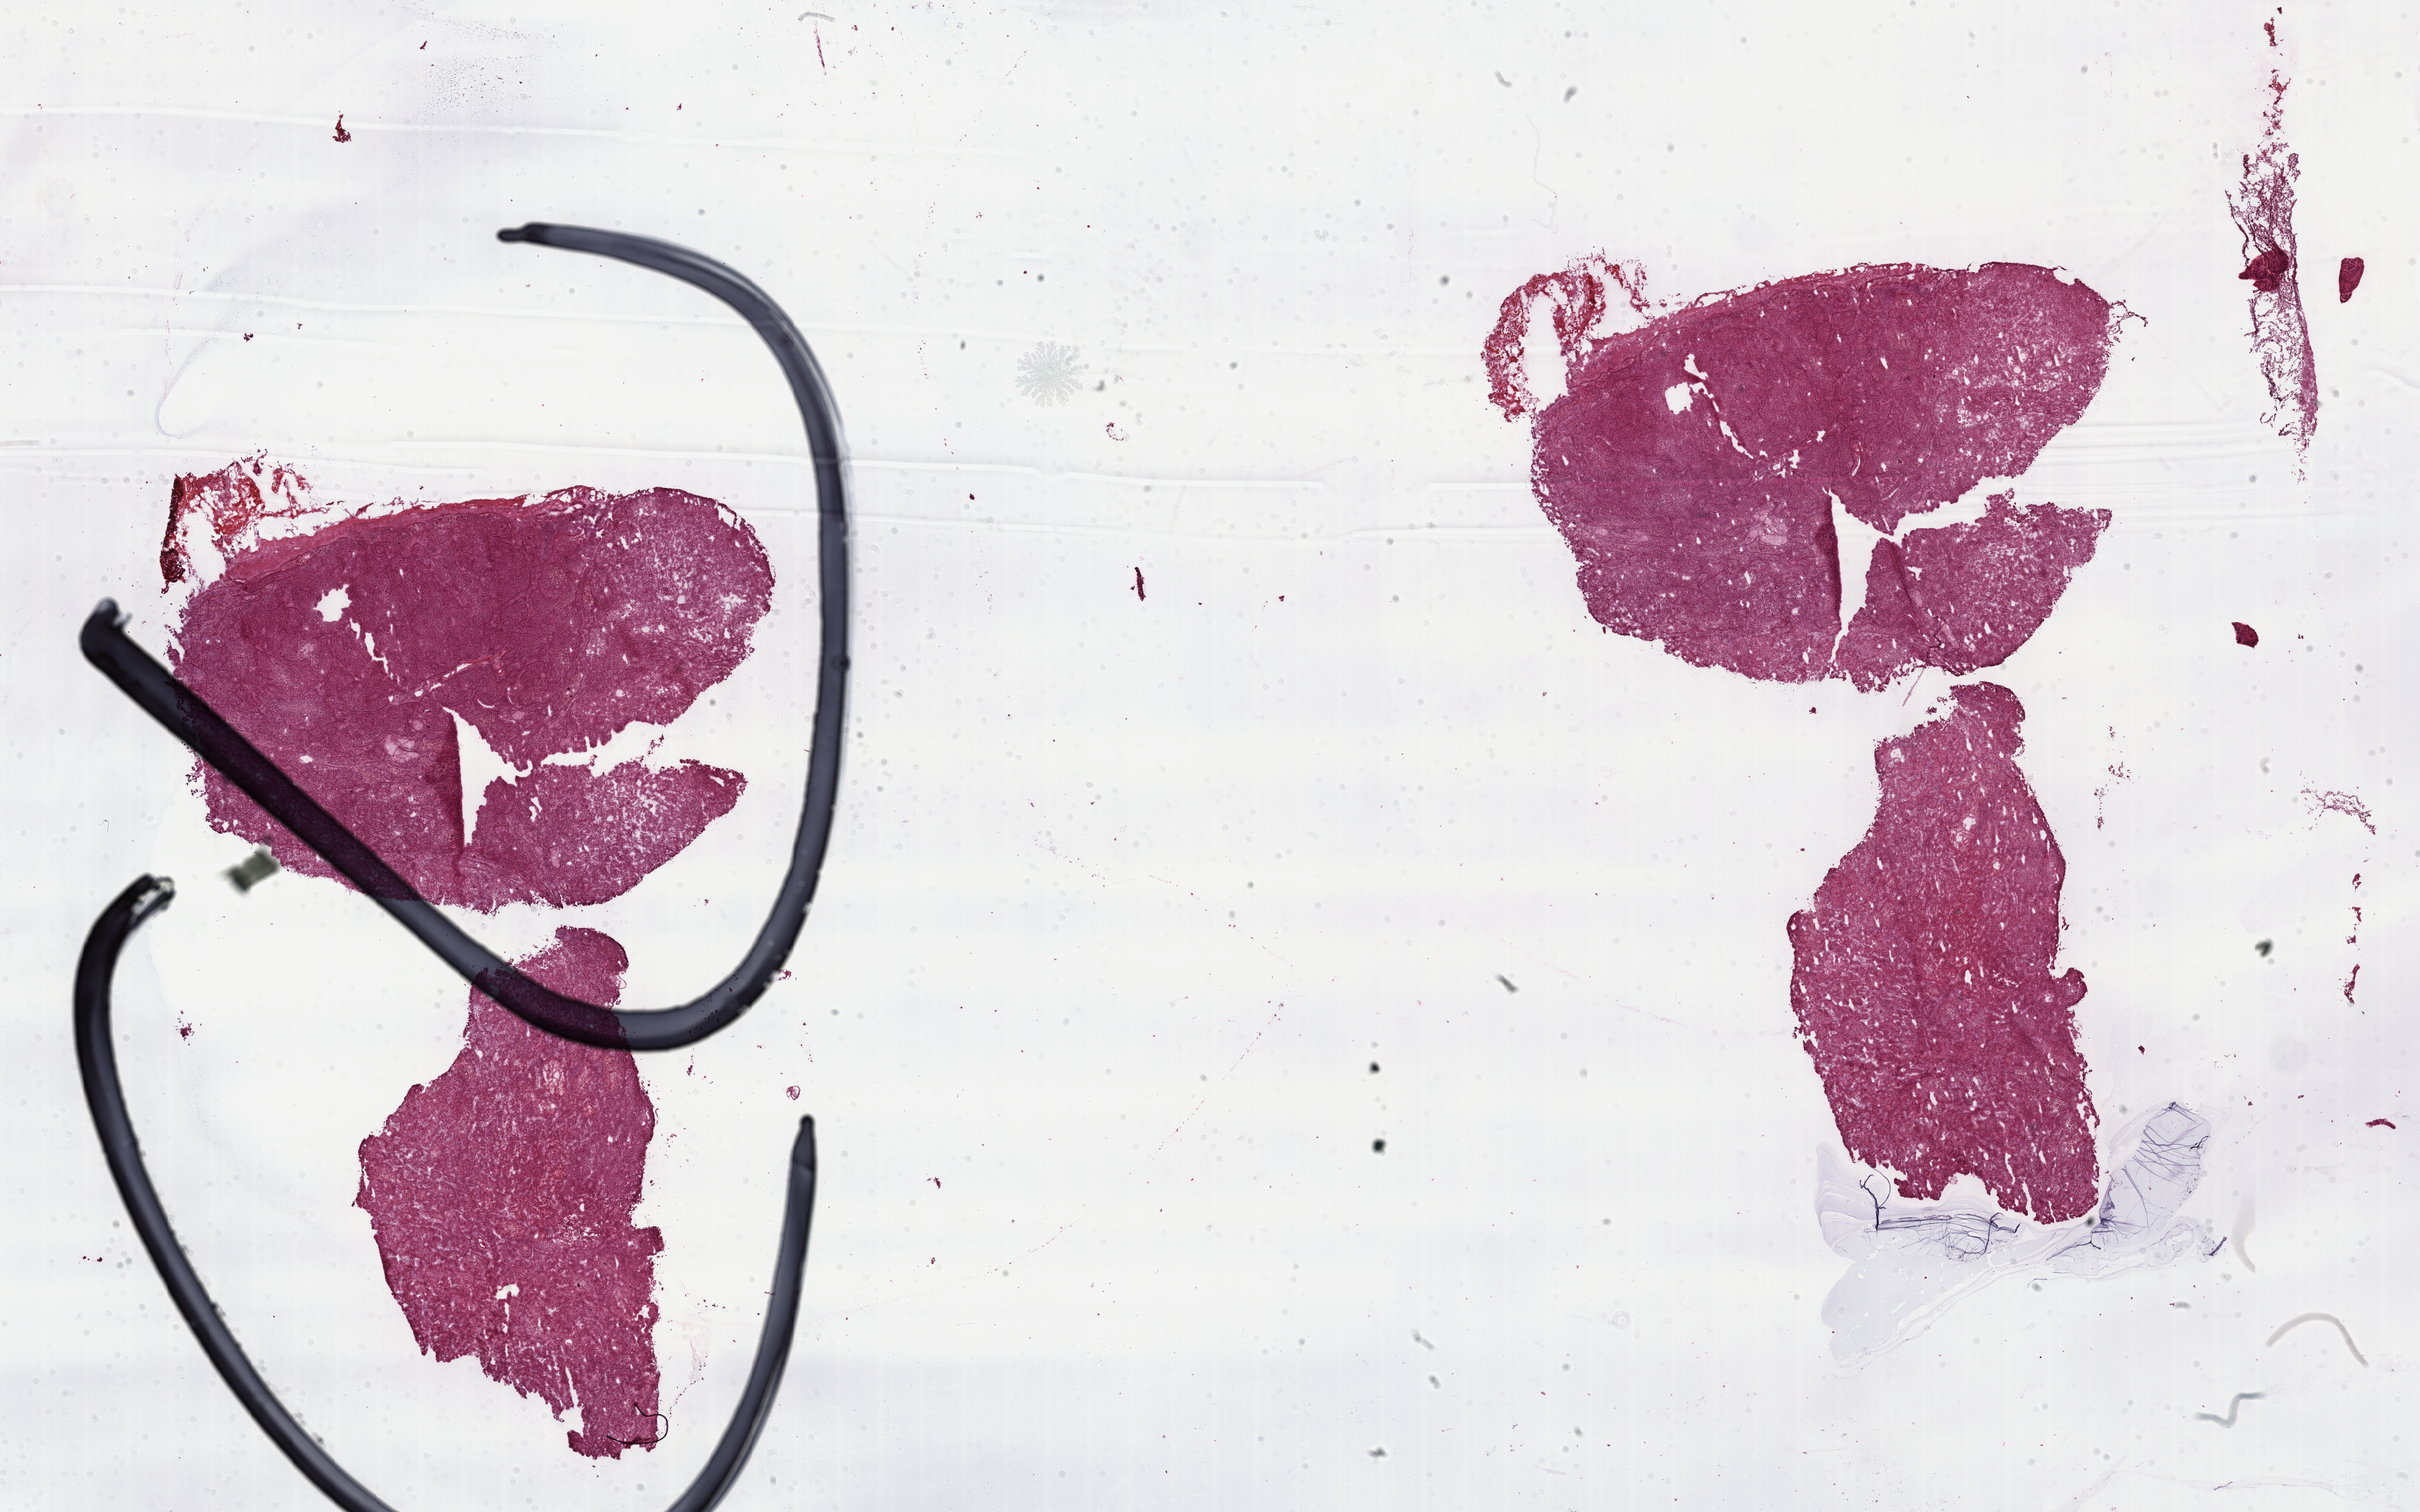
H&E whole-slide image, low-resolution overview of the scanned area, about 29.2 x 18.2 mm (acquisition: 40x scan); frozen section from the top of the tissue portion; sample: primary tumour, kidney. Male, age 61 years at initial diagnosis. Composition of this section per pathologist review: tumour cells 100%, tumour nuclei 70%, normal cells 0%, stromal cells 0%, necrosis 0%. Infiltration values recorded for this section: lymphocyte infiltration 2%, monocyte infiltration 5%, neutrophil infiltration 0%.
Pathologic diagnosis: Papillary adenocarcinoma, NOS.